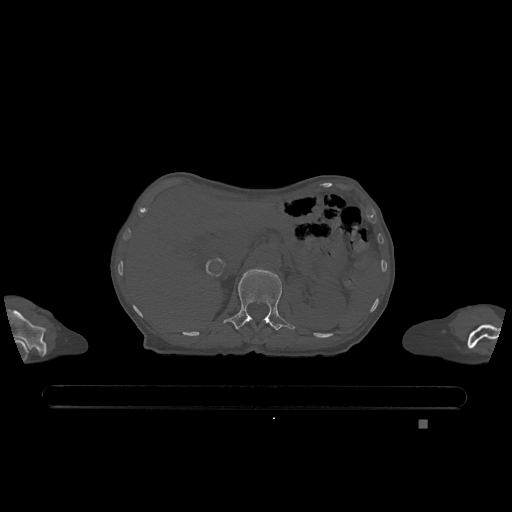
CT including the spine, one axial slice; bone window (W 1800 / L 400 HU); 0.5 mm slice thickness; 512 × 512 image matrix, field of view 500 × 500 mm. Female patient, age 74 years. From the clinical record (not read from this slice): primary cancer: lung.
Outlined on this slice (semi-automatically segmented with operator editing):
- L1 vertebra: bounding box [x1, y1, x2, y2] px = [223, 268, 295, 331]